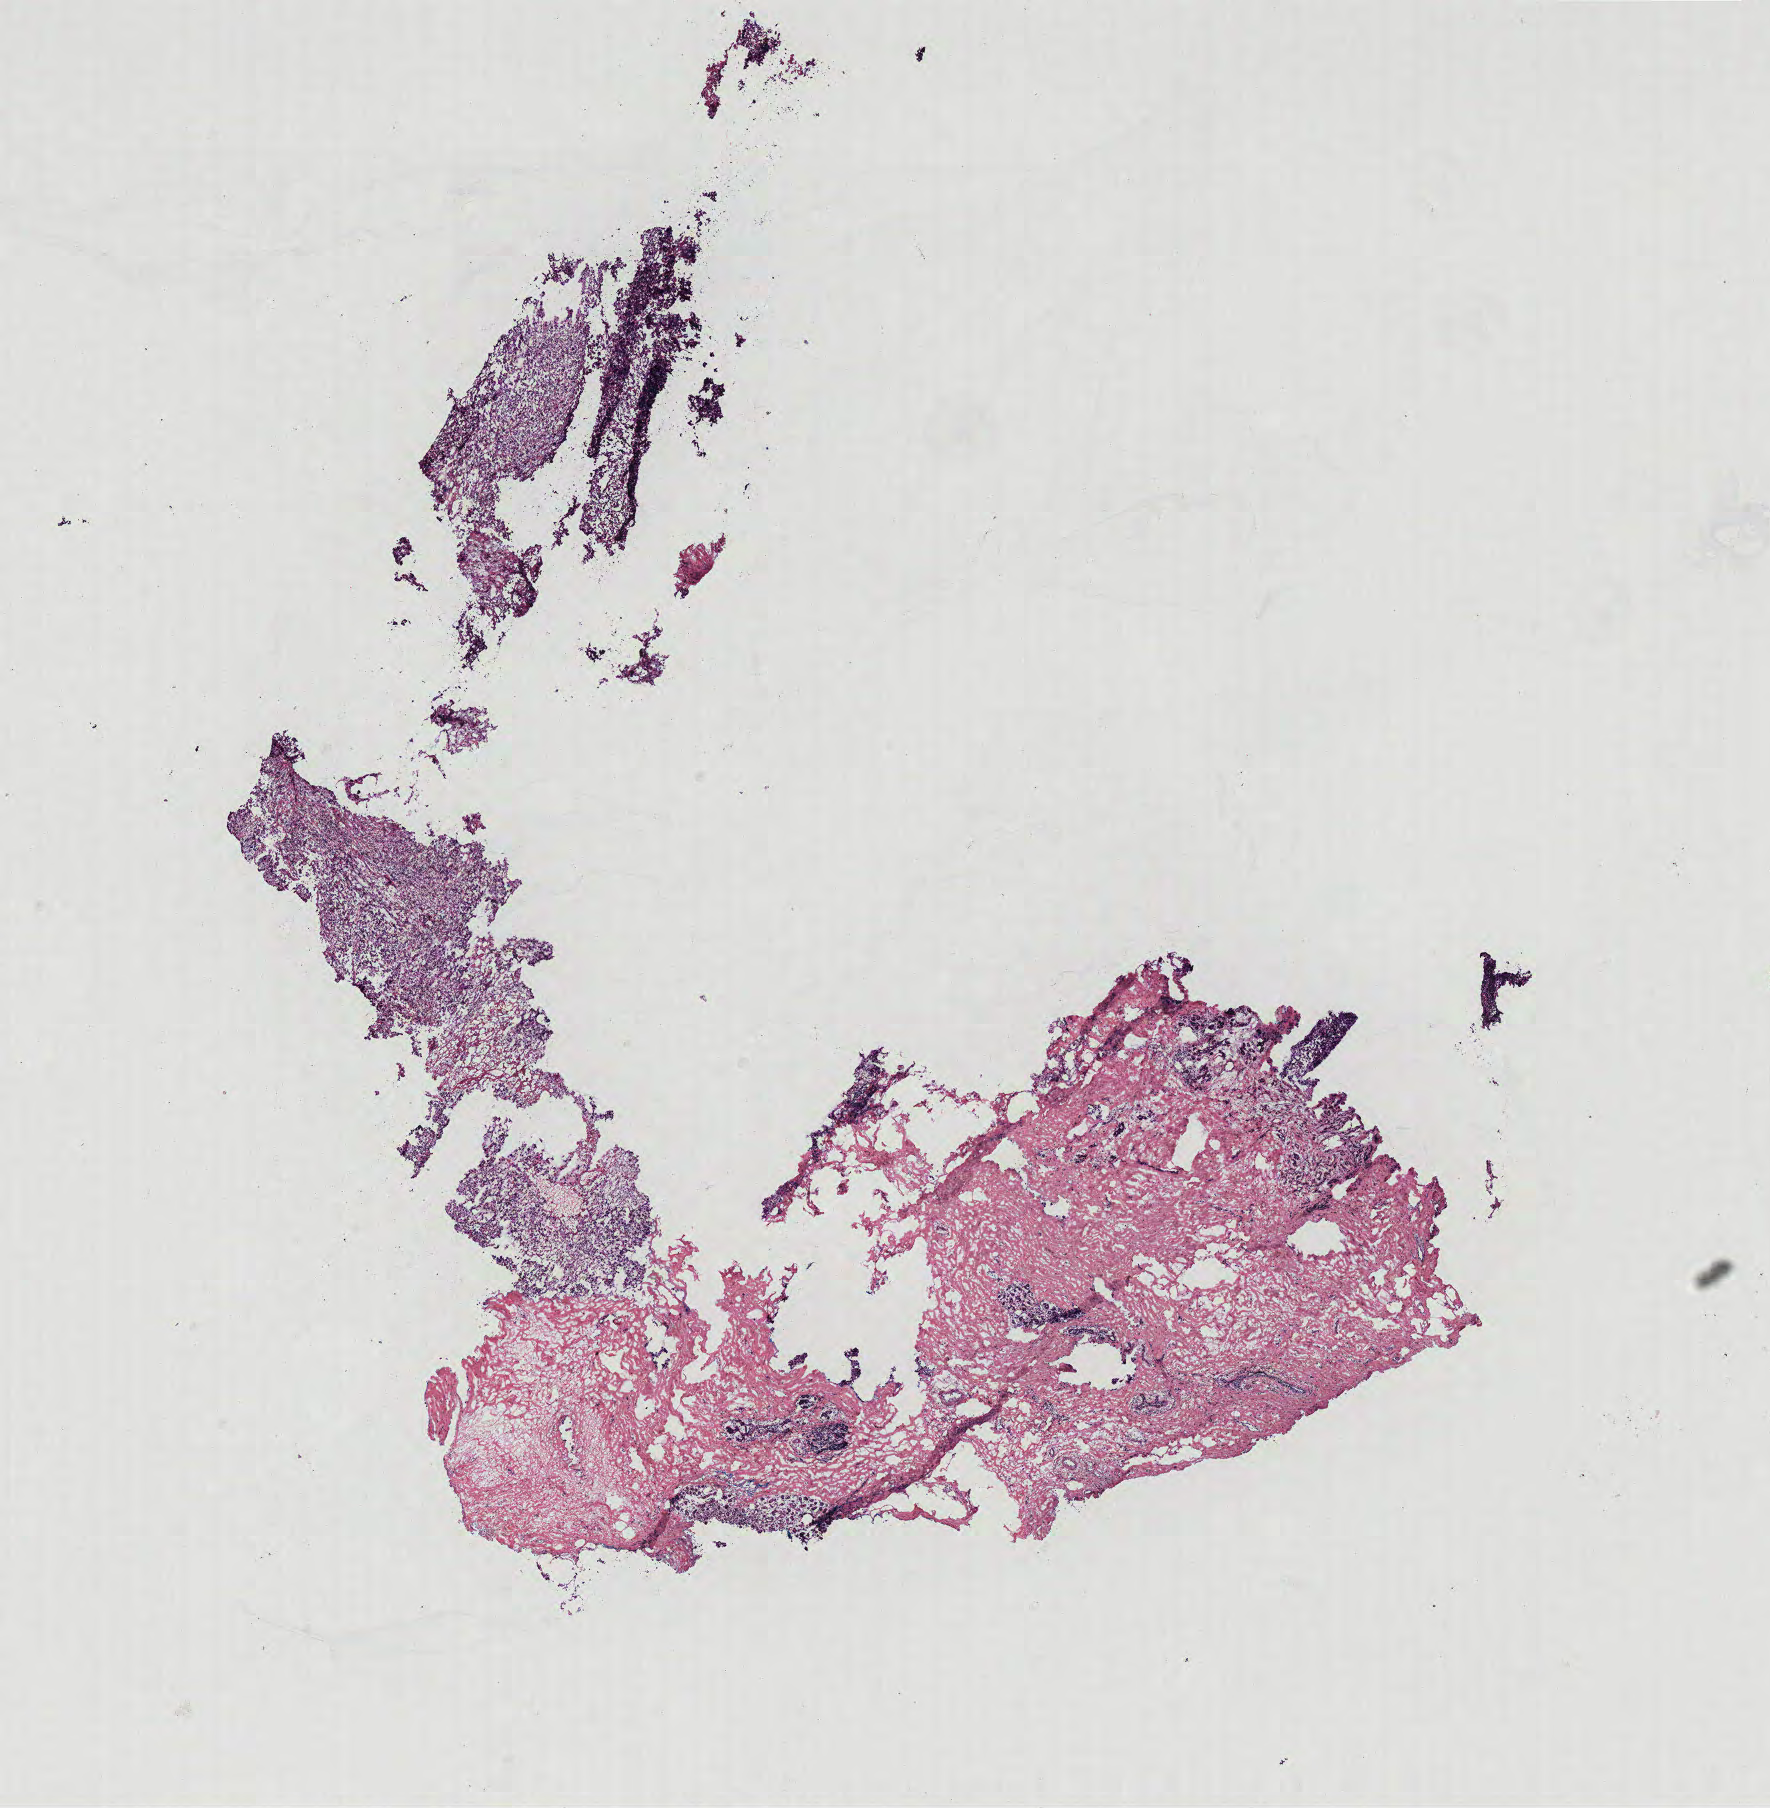
Whole-slide histology image, H&E-stained, a low-resolution overview of the entire scanned area, about 14.2 x 14.5 mm, breast, tissue type not recorded.
* patient diagnosis (cohort enrolment): breast cancer (breast)